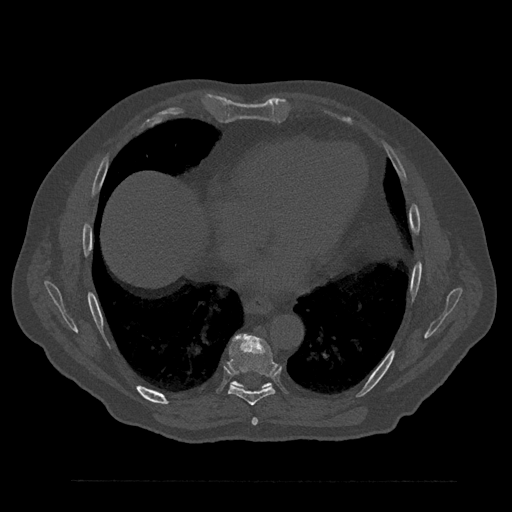
CT including the spine, one axial slice; position 445 of 797 along the scan axis; reconstruction kernel Br40s/3; 120 kVp; bone window (W 1800 / L 400 HU); 0.5 mm slice thickness; 512 × 512 image matrix, field of view 430 × 430 mm. Male patient, age 61 years. Case-level facts recorded for this patient, not image findings: primary cancer: prostate.
Structures marked on this image (semi-automatic segmentation, software-assisted and operator-edited):
- T7 vertebra: bounding box [x1, y1, x2, y2] px = [252, 418, 258, 425]
- T8 vertebra: [227, 335, 278, 406]
- T9 vertebra: [232, 381, 271, 388]